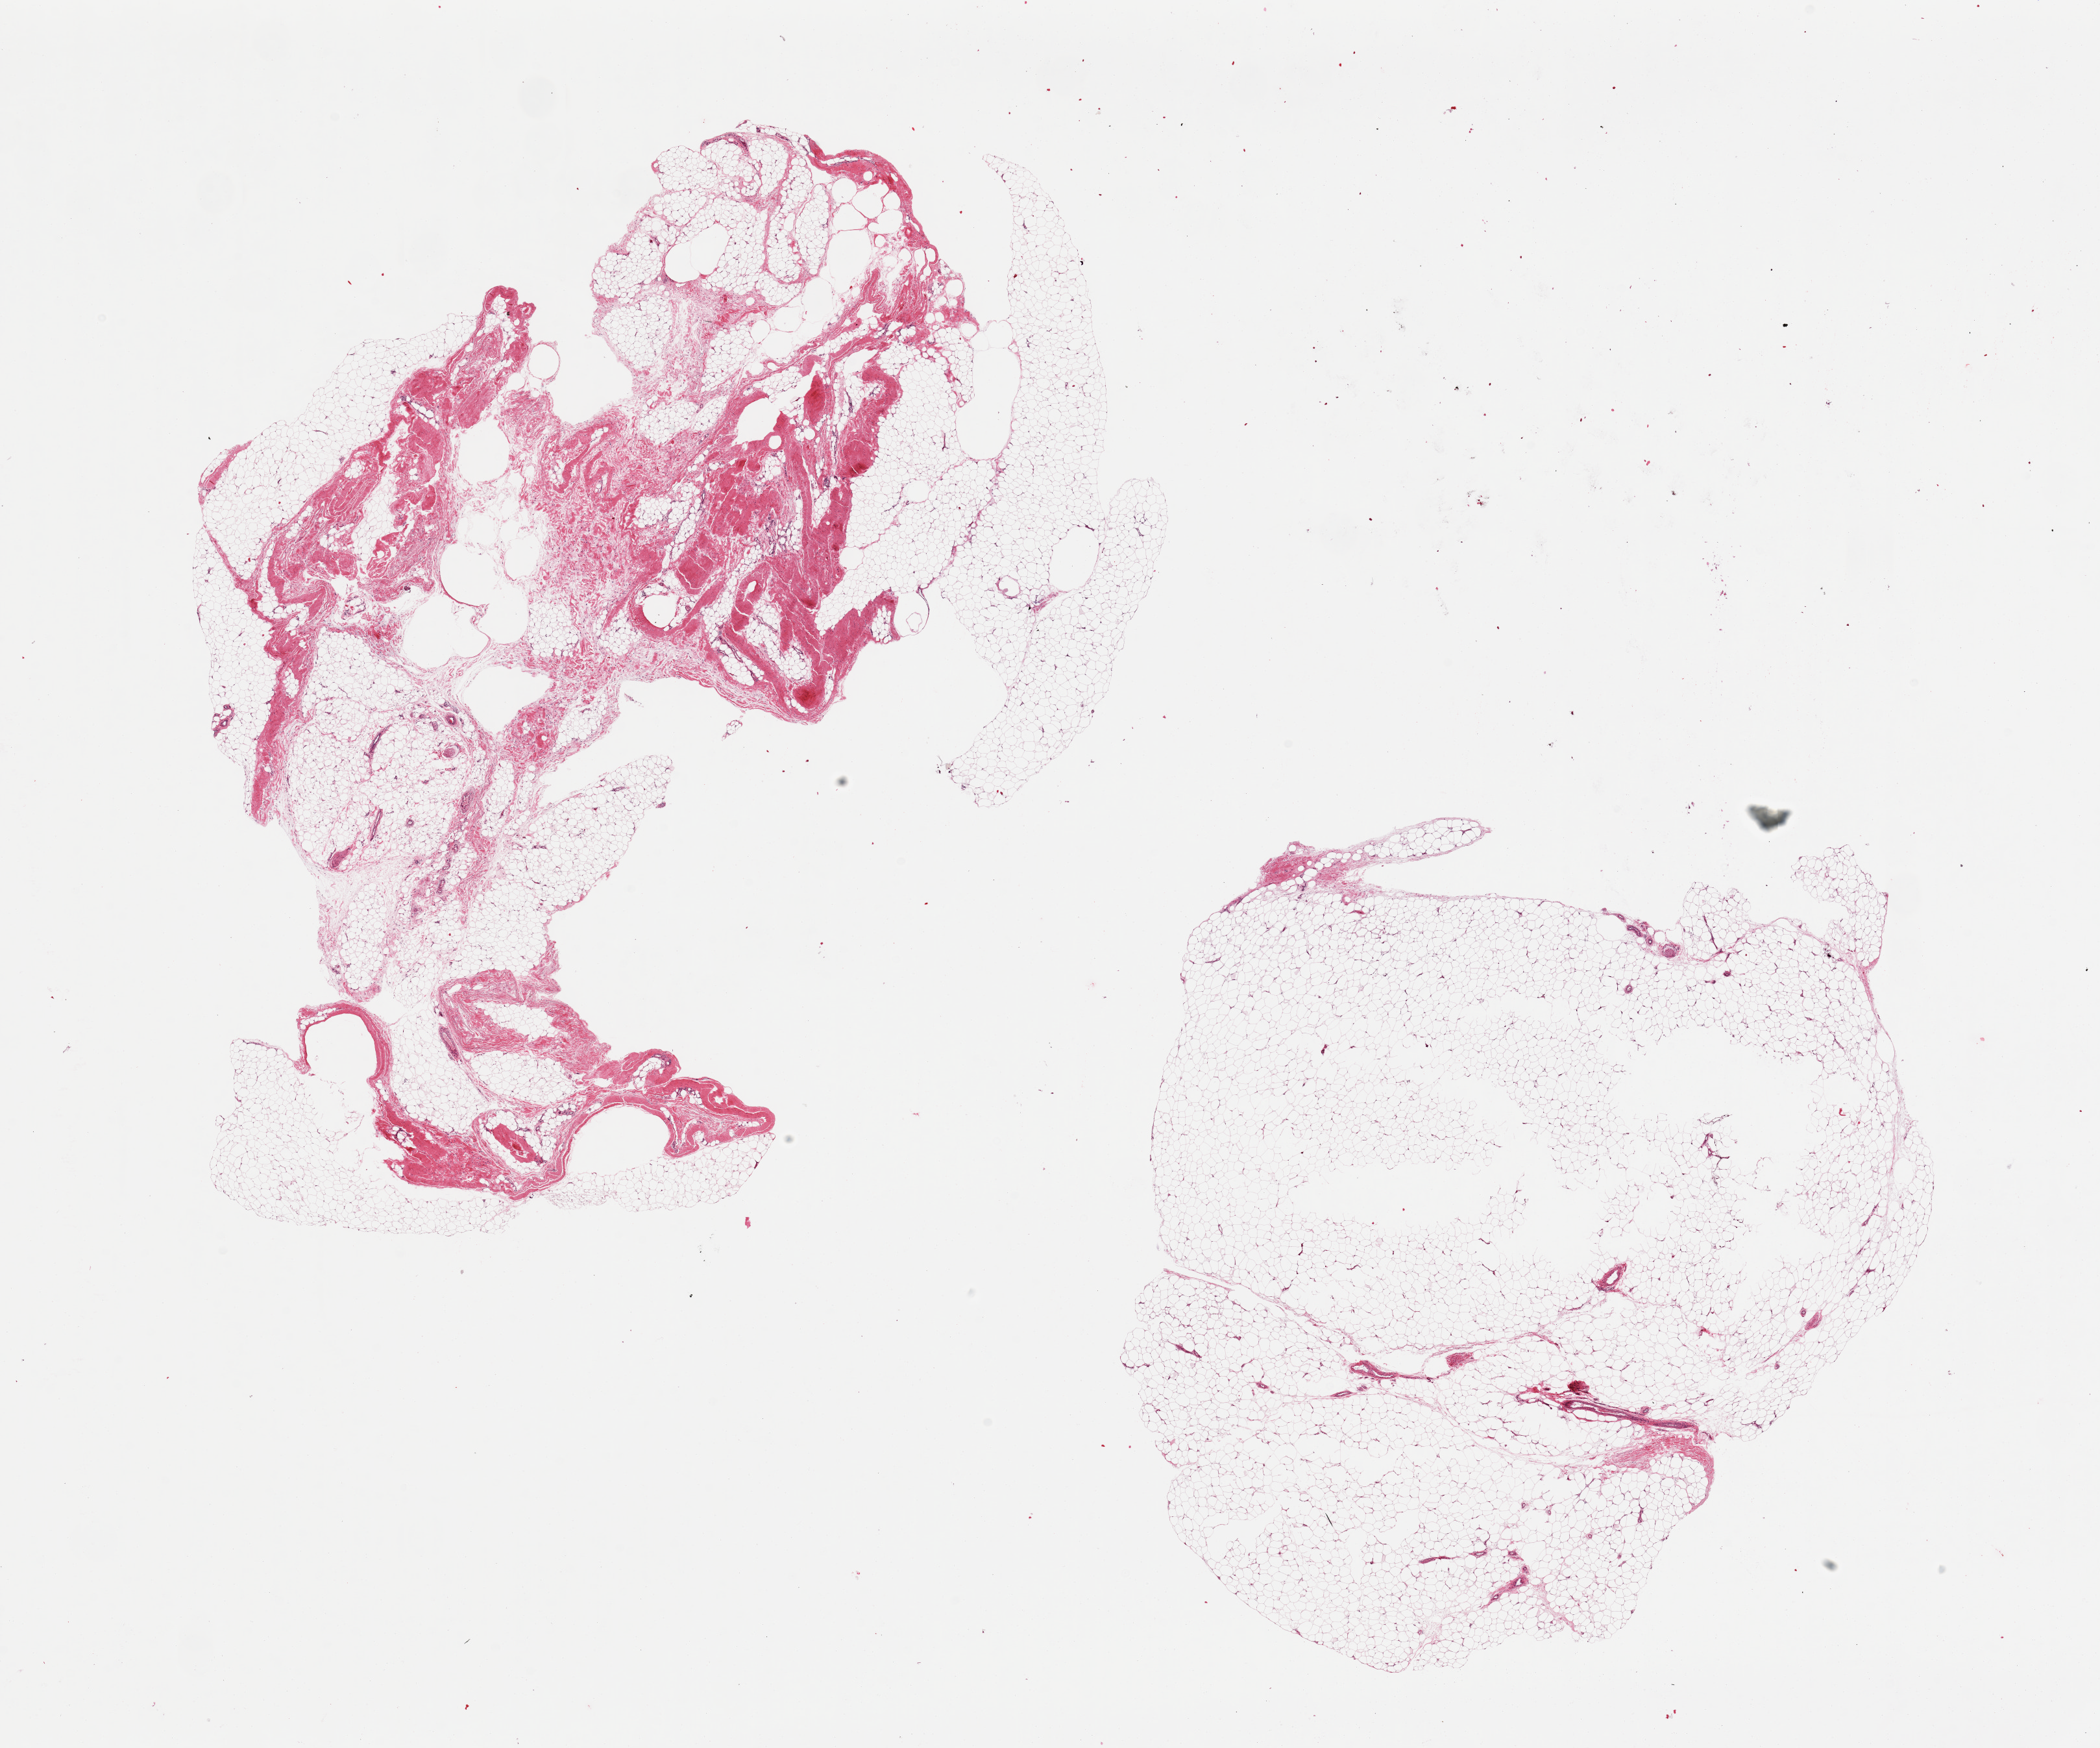
Haematoxylin and eosin whole-slide image — low-resolution overview of the scanned area, about 25.6 x 21.3 mm. PAXgene-fixed paraffin-embedded (PFPE) section. Sampled site (target tissue): adipose tissue. Donor tissue sample. Female donor.
Pathologist's review note for this sample: 2 pieces, both with some central defects suggesting incomplete fixation. One piece predominantly fat, second is 50% fibroconnective tissue.